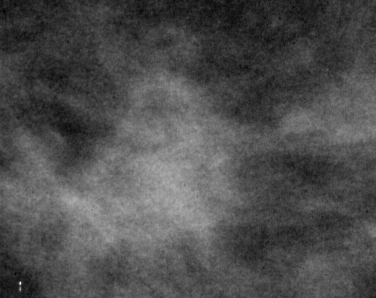
Crop from a digitized film mammogram around one marked abnormality; right breast; MLO view; BI-RADS breast density category 2 (scale 1–4).
- Finding: mass, shape irregular, margins spiculated; BI-RADS assessment category 5; subtlety rating 2 on a 1 (subtle) to 5 (obvious) scale; pathology result (as recorded, not read from the image): malignant.